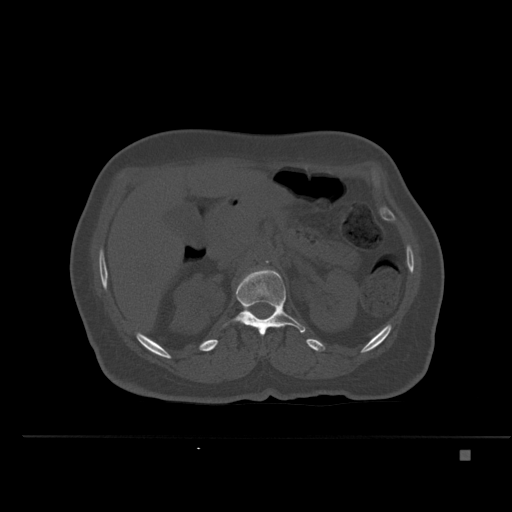
CT including the spine, one axial slice; position 235 of 477 along the scan axis; bone window (W 1800 / L 400 HU); 1.5 mm slice thickness; 512 × 512 image matrix. Female patient, age 74 years. Case-level facts recorded for this patient, not image findings: primary cancer: colon.
Outlined on this slice (semi-automatically segmented with operator editing):
- L1 vertebra: bounding box <224,268,306,336> (left, top, right, bottom; pixels)